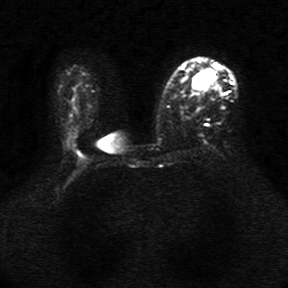
Breast MRI, one axial slice. Slice 21 of 34 in the series (ordered by position). Diffusion-weighted series; image 2 of 4 stored at this slice position (different b-values; order by instance number). 1.5 T. 5 mm slice thickness. 288 × 288 image matrix, field of view 340 × 340 mm. Female patient.
Structures marked on this image (outlined manually by an expert reader):
- tumour on diffusion-weighted imaging: bounding box [x1, y1, x2, y2] px = [193, 74, 206, 88]